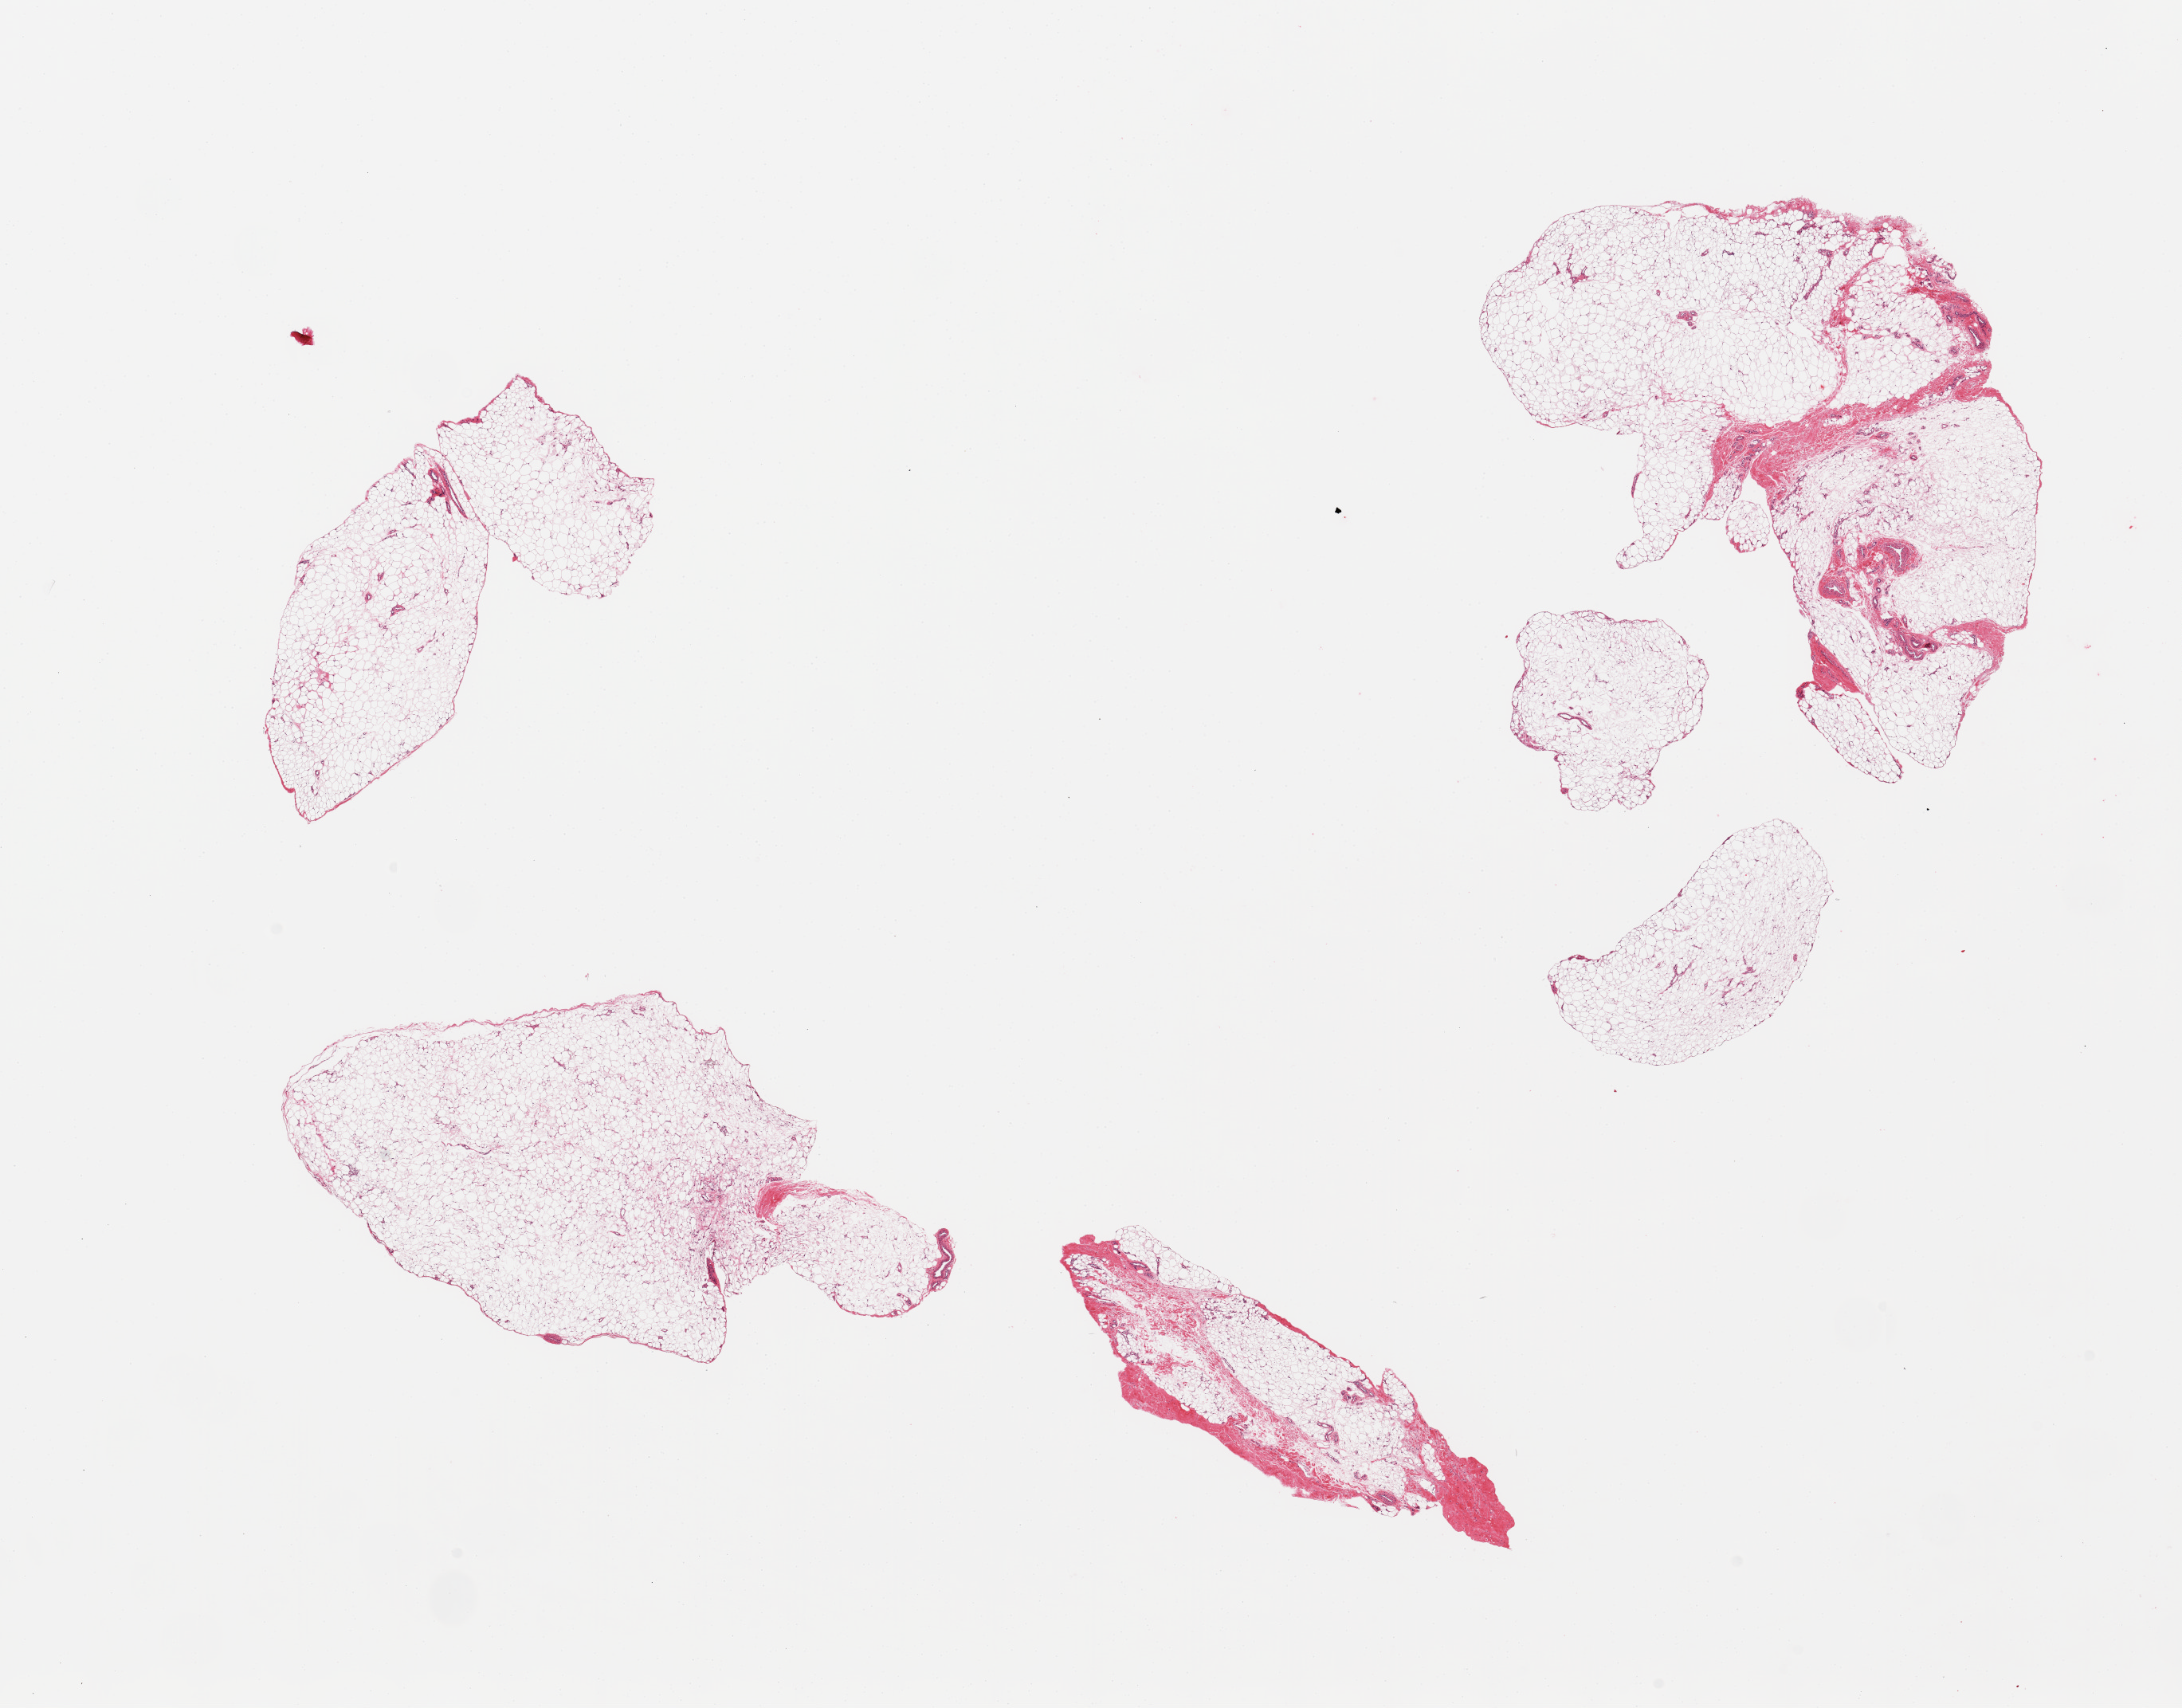
Digitized haematoxylin and eosin-stained section — shown as a low-resolution overview of the whole scanned area (about 21.7 x 17.0 mm, from a 20x scan); PAXgene-fixed paraffin-embedded (PFPE) section; target tissue: adipose tissue; donor tissue sample. Donor: male.
Review note (as recorded): several fragmented pieces.